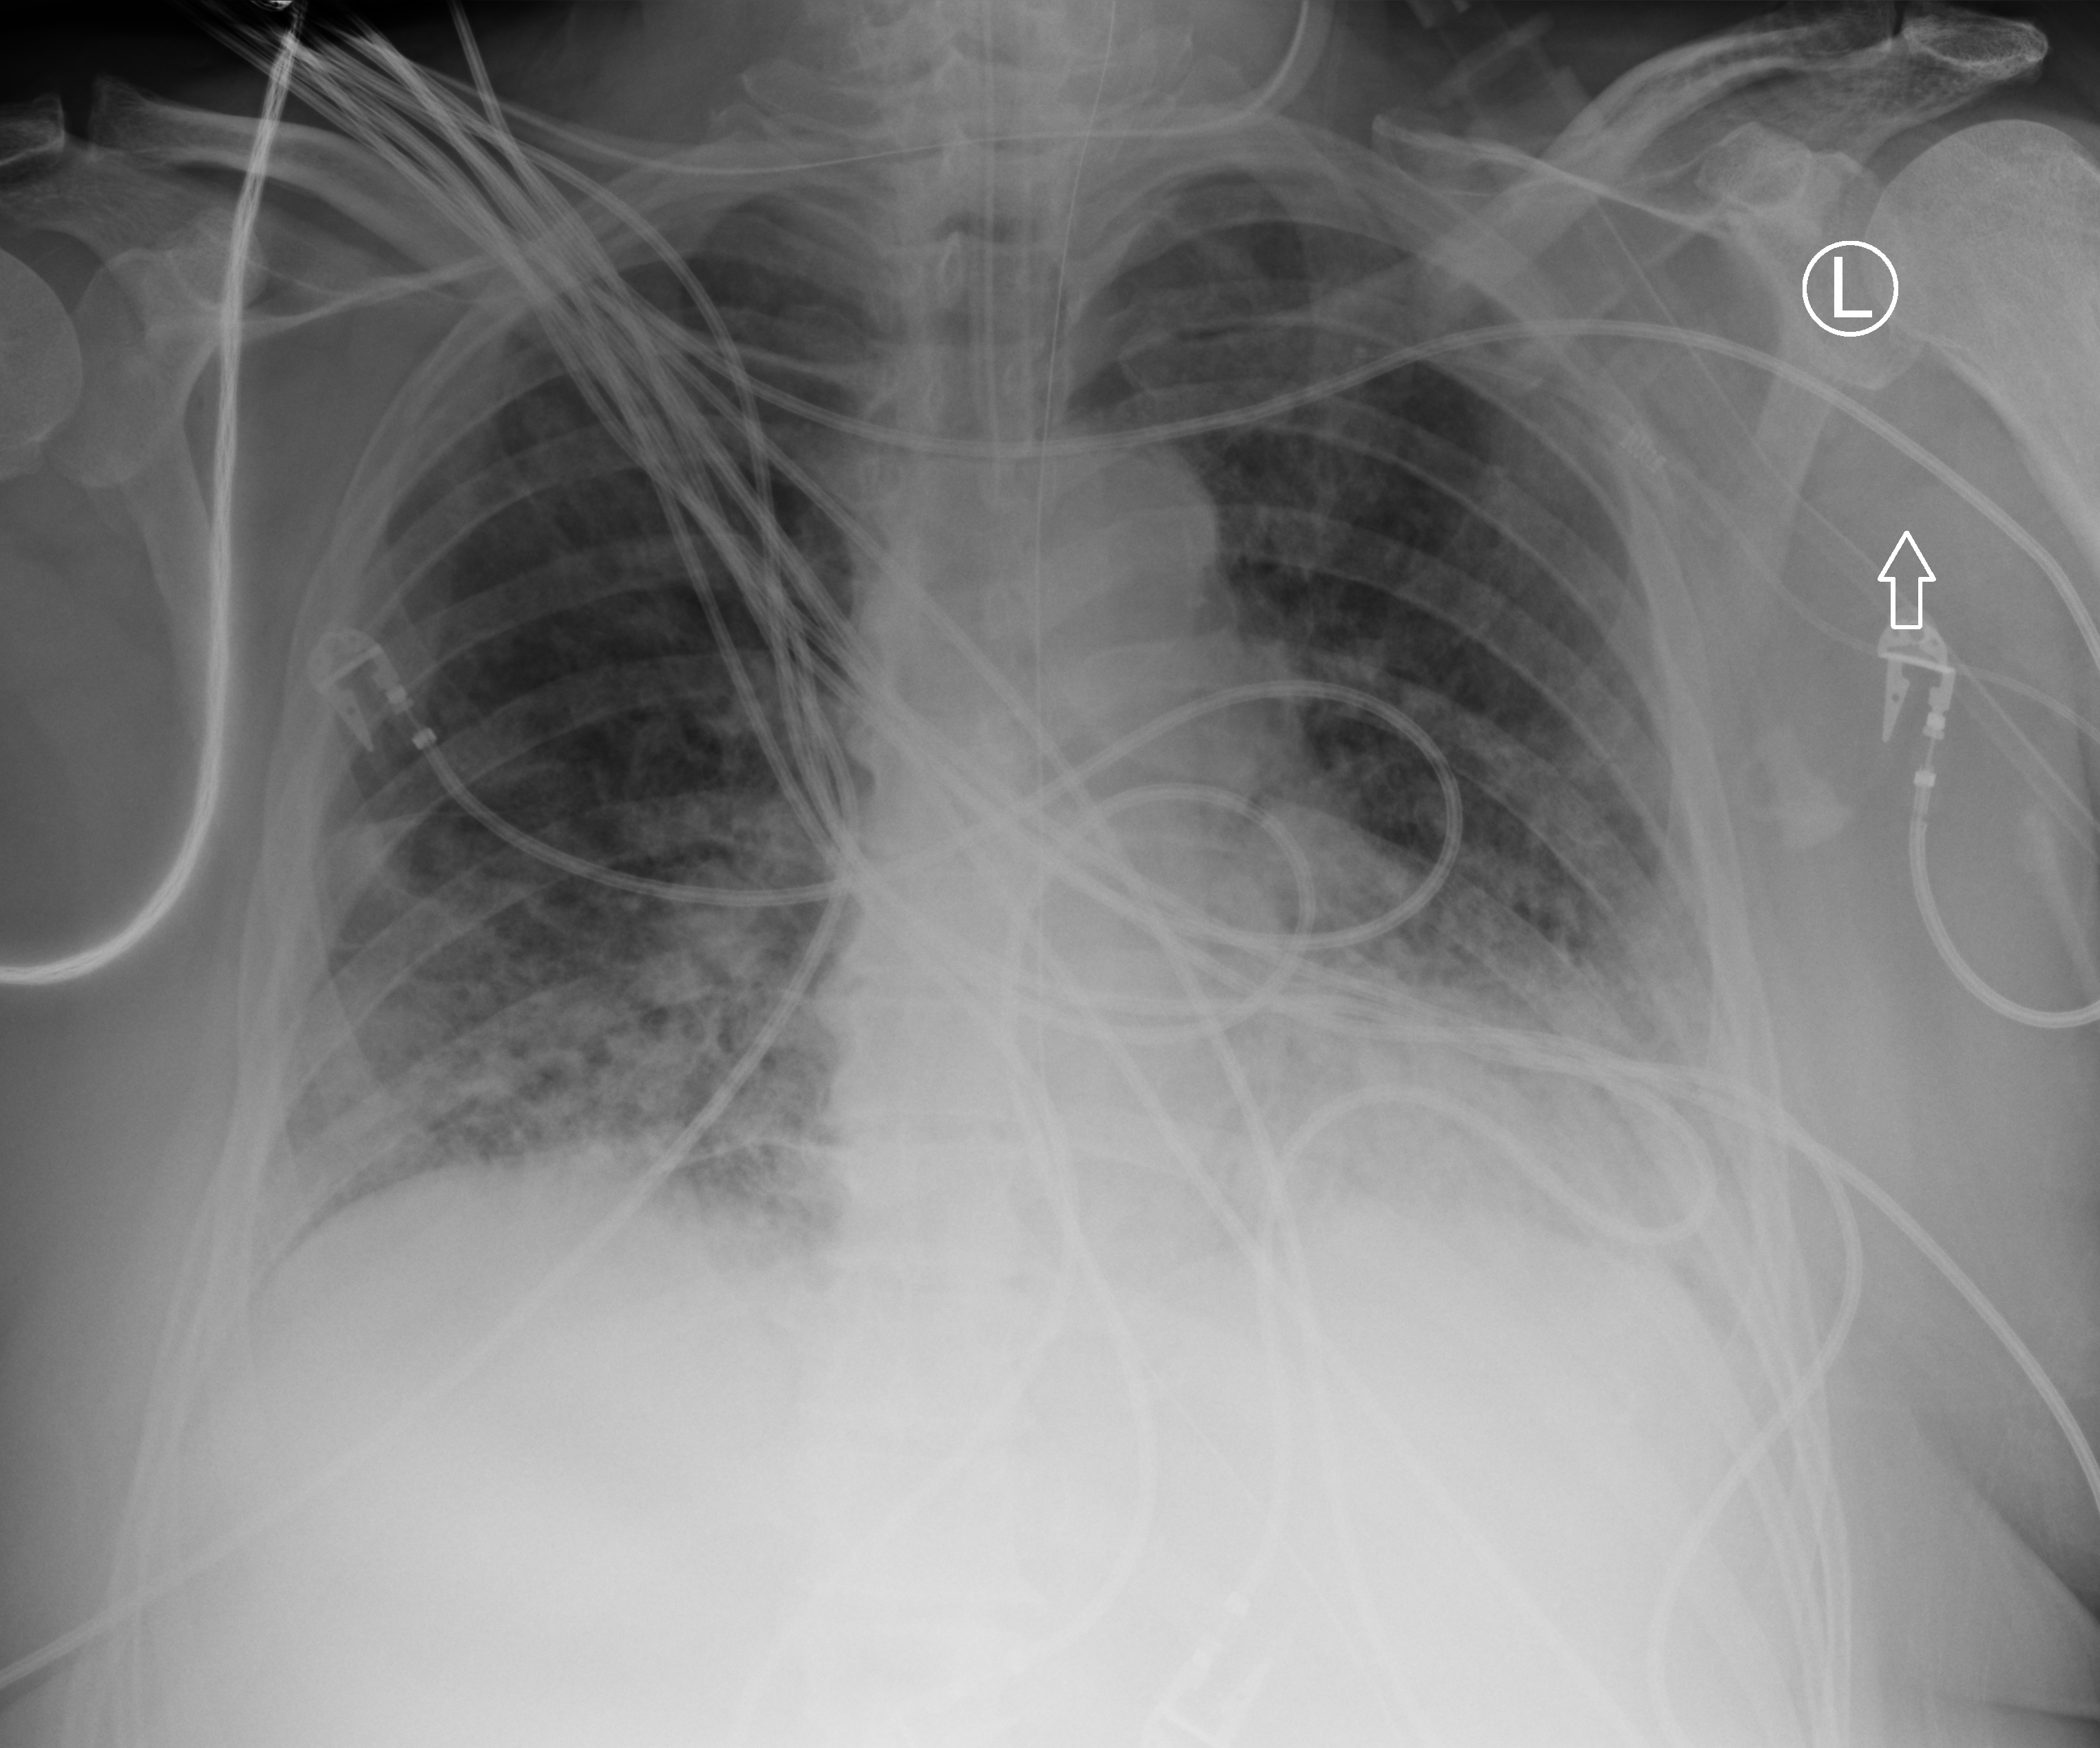
Portable chest radiograph; anteroposterior (AP) projection. Male patient hospitalised with COVID-19, age 60–74 years.
Hospital-stay facts (about this admission, not read from this image; timing relative to this image not recorded): admitted to intensive care during this hospital stay: yes.